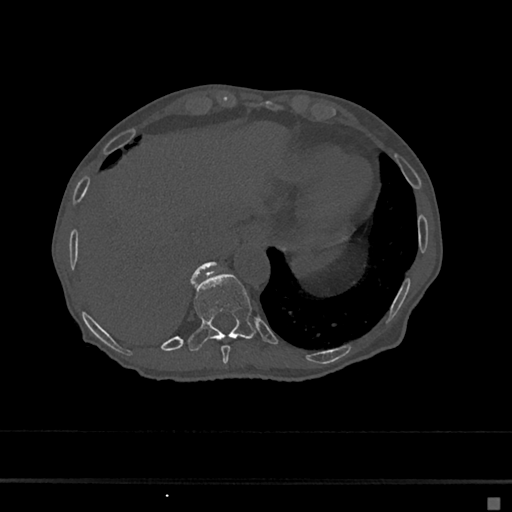
CT including the spine, one axial slice; position 232 of 797 along the scan axis; reconstruction kernel Br40s/3; 120 kVp; bone window (W 1800 / L 400 HU); 0.5 mm slice thickness; 512 × 512 image matrix, field of view 360 × 360 mm. Female patient, age 68 years. From the clinical record (not read from this slice): primary cancer: renal.
Structures marked on this image (semi-automatically segmented with operator editing):
- T10 vertebra: bounding box (x1, y1, x2, y2) in pixels: (188, 273, 256, 351)
- T11 vertebra: (192, 261, 218, 279)
- T9 vertebra: (221, 345, 231, 364)